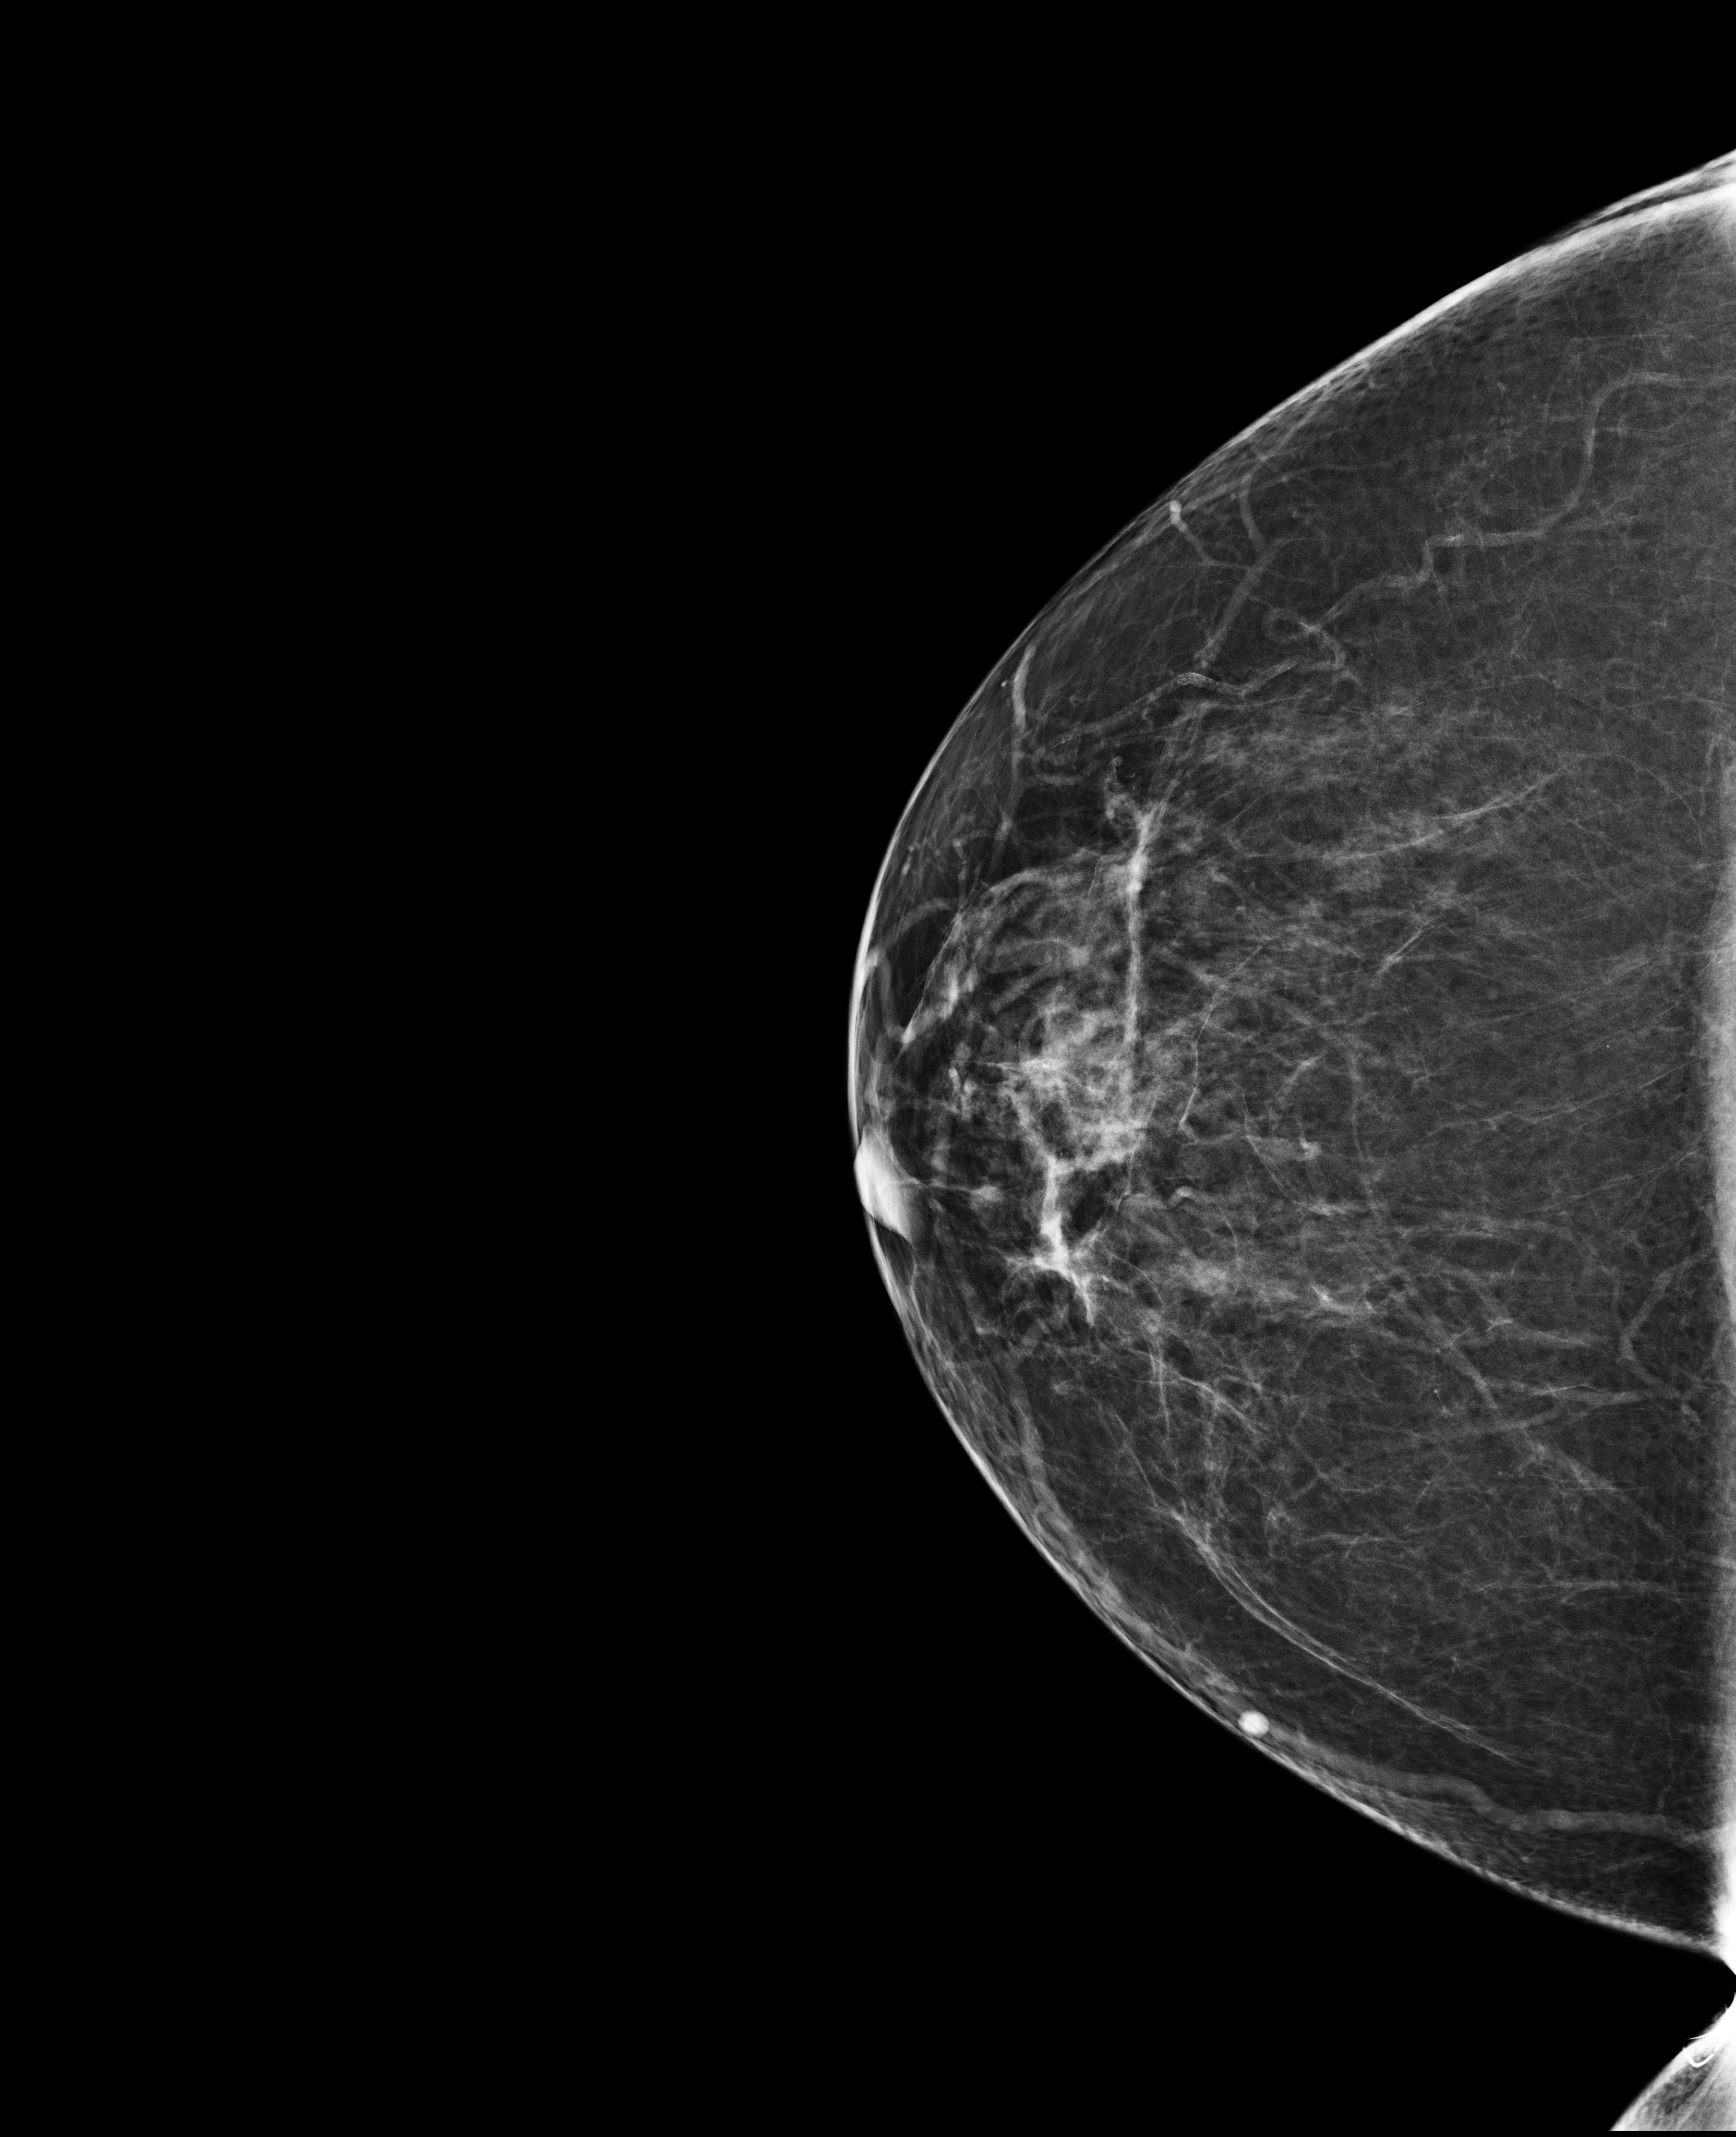
Full-field digital mammogram (FFDM), right breast, cranio-caudal projection, screening examination, compressed breast thickness 74 mm, system: Selenia Dimensions. Female patient, age 61 years.
BI-RADS breast density category at the screening exam (both breasts, scale 1–4): 3. Final BI-RADS assessment for this screening round (tomosynthesis exam, both breasts): category 1. Recall: no recall after this screen.